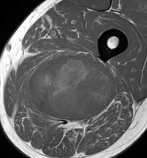
MRI of an extremity soft-tissue mass, one axial slice; slice 65 of 86 in the series (ordered by position); MR volume resampled by the dataset authors to the PET/CT grid (not the native acquisition matrix); 3.27 mm slice thickness; 147 × 158 image matrix. Male patient. Case-level facts recorded for this patient, not image findings: histological type: undifferentiated pleomorphic liposarcoma; grade: high; site of the primary tumour: left thigh.
Structures marked on this image (expert contour drawn on MRI and transferred to this co-registered scan by the dataset authors):
- gross tumour volume including surrounding oedema: bounding box [x1, y1, x2, y2] px = [18, 54, 115, 130]
- gross tumour volume (mass): [26, 54, 115, 120]